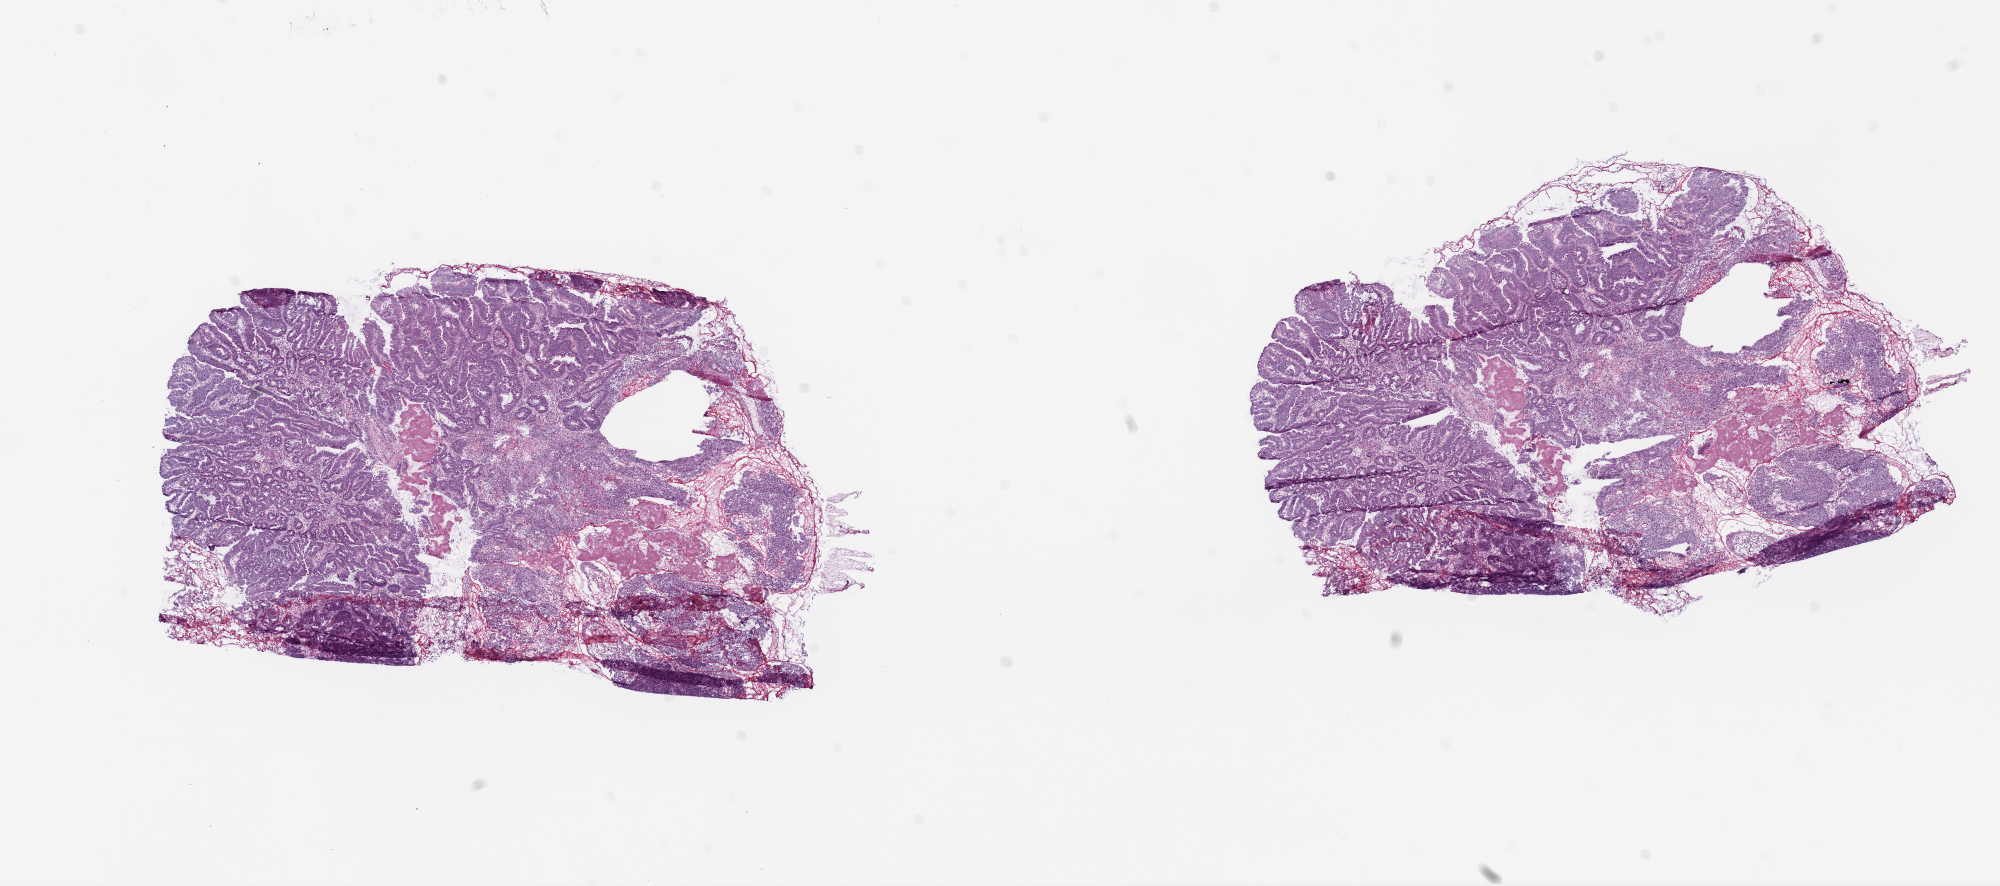
Digitized Hematoxylin and eosin (H&E) stained tissue section (whole slide), whole scanned area (about 16.0 x 7.1 mm, acquisition: 20x scan) shown as a low-resolution overview, frozen section, rectum, primary tumour sample. Patient: female, age at initial diagnosis 57 years. Composition of this section per pathologist review: tumour cells 85%, tumour nuclei 75%, normal cells 0%, stromal cells 12%, necrosis 3%.
Pathologic diagnosis: Adenocarcinoma, NOS. TNM: T1 N0 M0. AJCC pathologic stage: I (6th edition). Lymph nodes positive (case pathology): 0 of 17 examined.